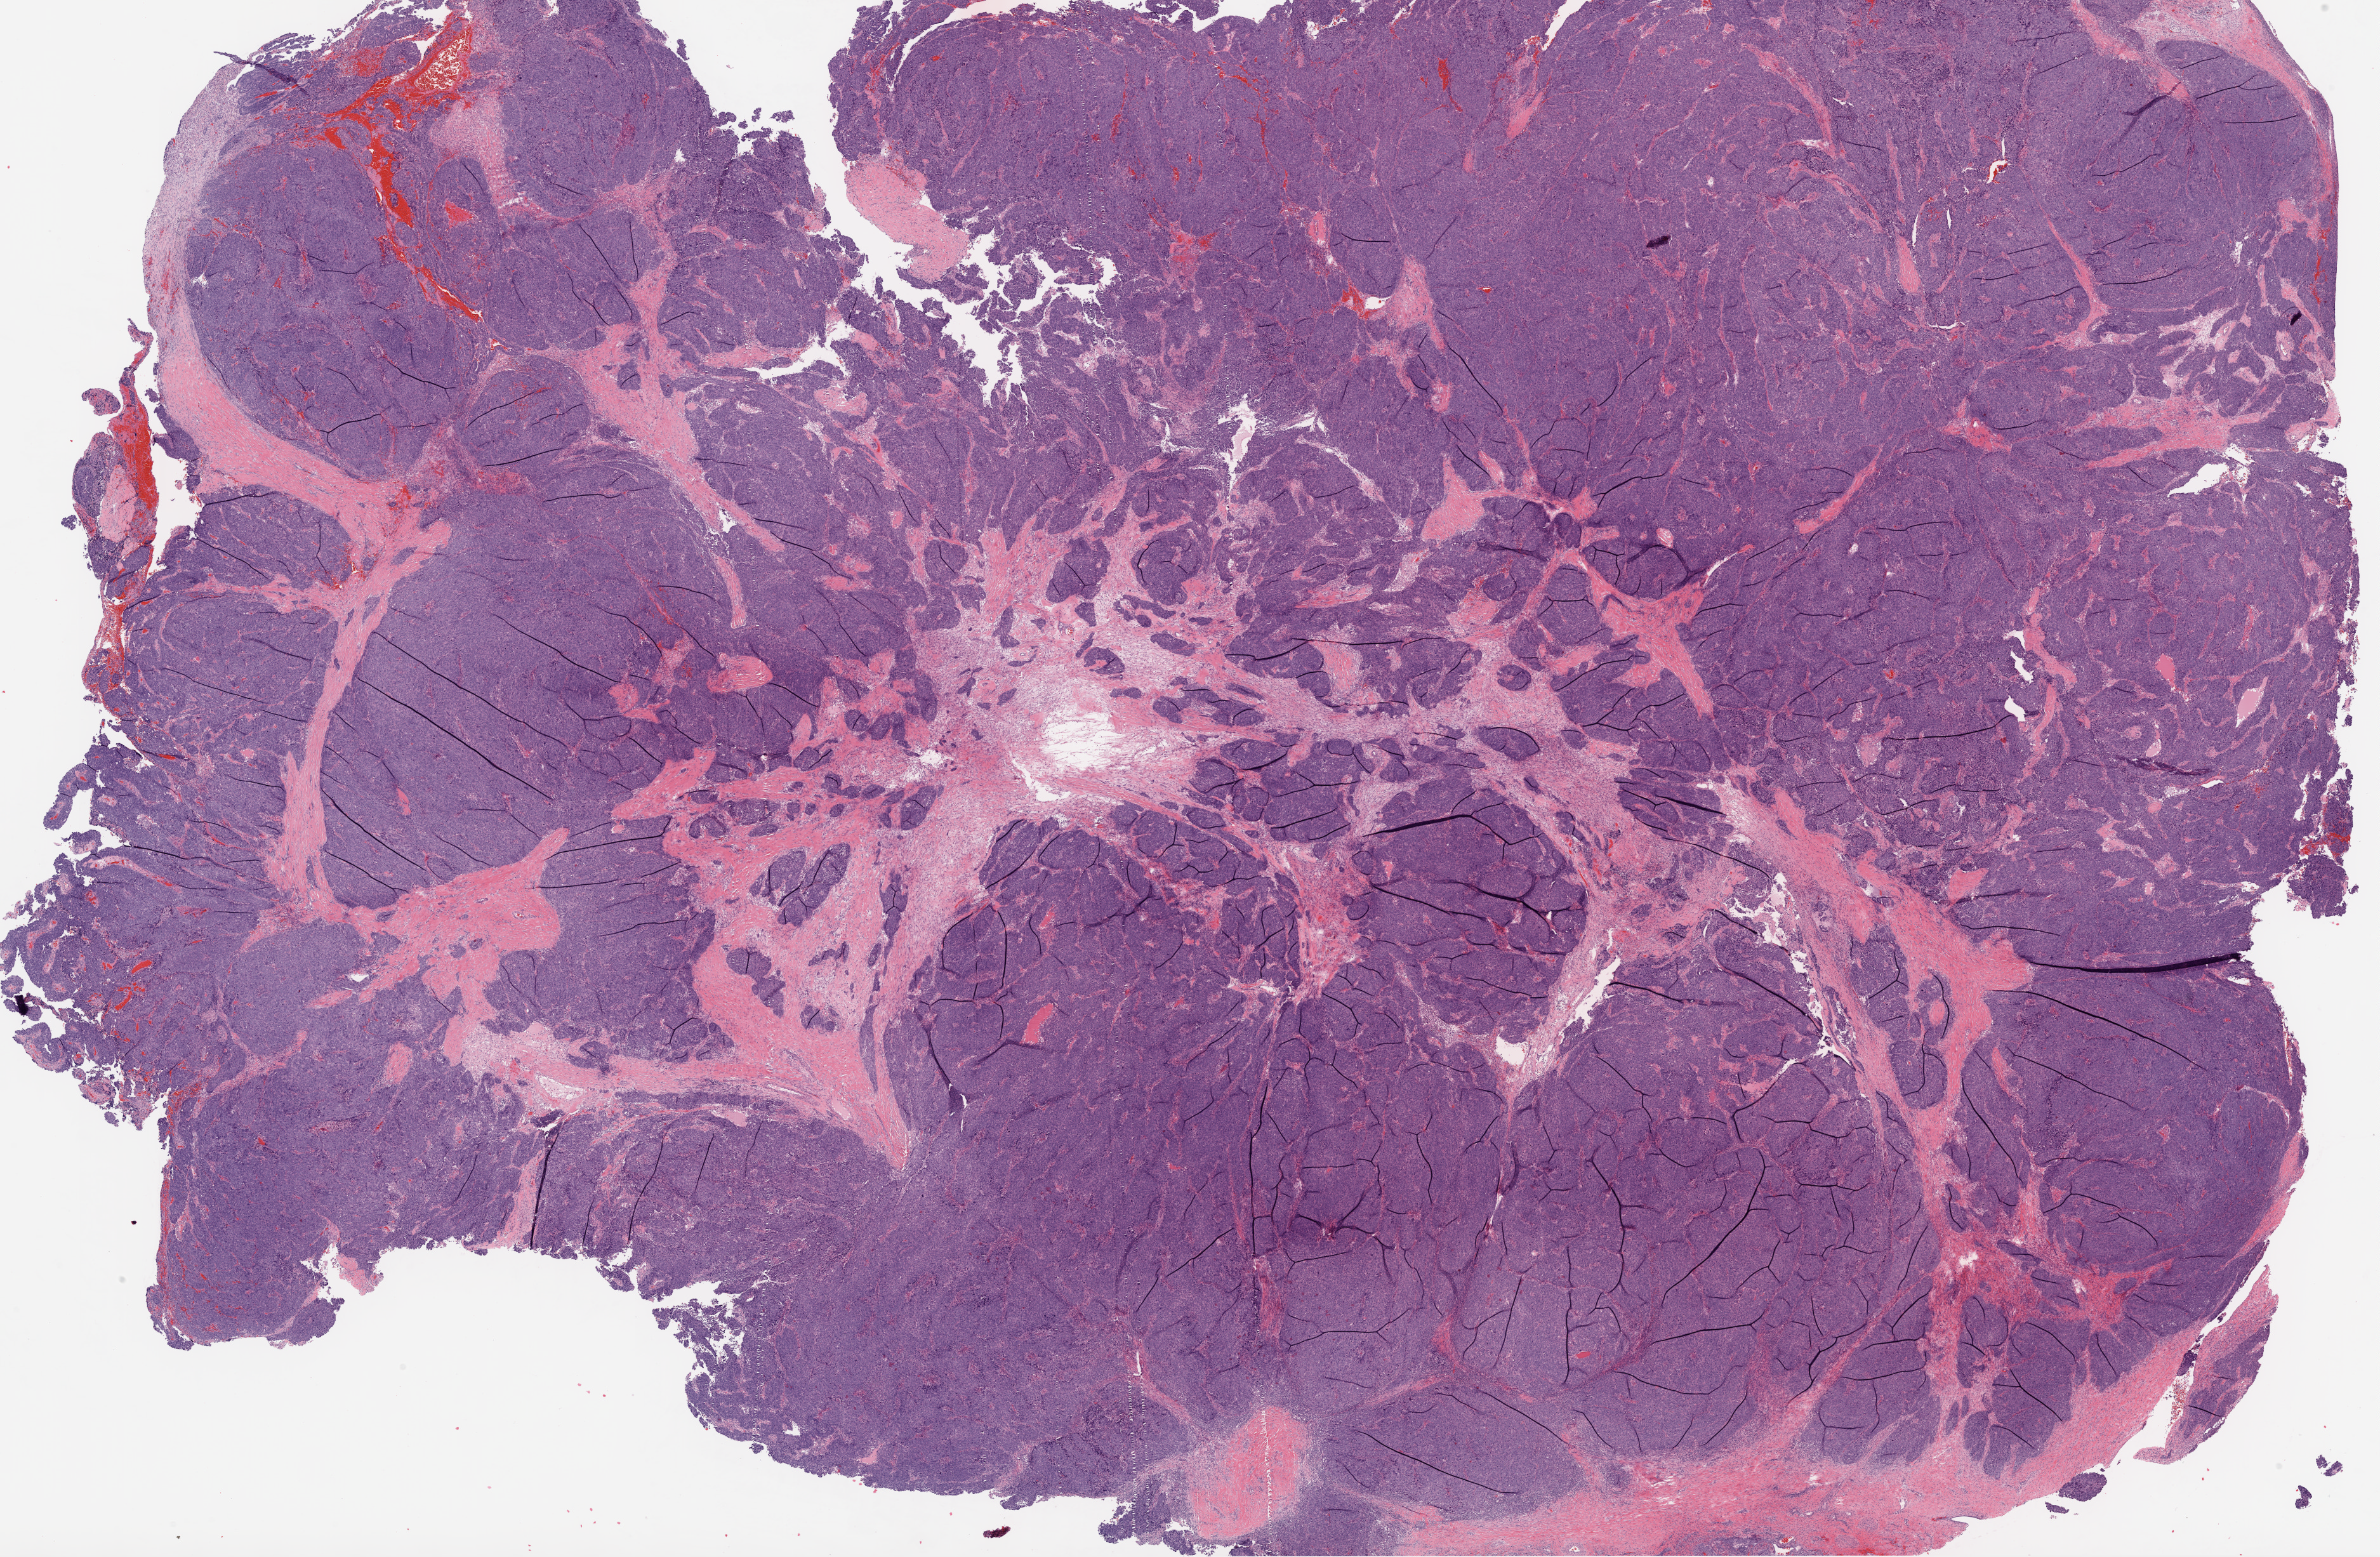
H&E-stained whole-slide image — whole scanned area (about 30.1 x 19.7 mm, acquisition: 20x scan) shown as a low-resolution overview; frozen section; sample: primary tumour, ovary. Female patient; age at initial diagnosis 42 years.
Diagnosis: Serous cystadenocarcinoma, NOS.